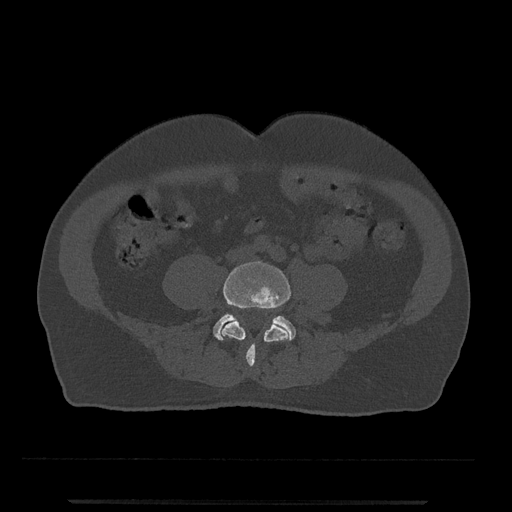
CT including the spine, one axial slice. Position 111 of 797 along the scan axis. 120 kVp. Bone window (W 1800 / L 400 HU). 0.5 mm slice thickness. 512 × 512 image matrix, field of view 419 × 419 mm. Male patient, age 63 years. From the clinical record (not read from this slice): primary cancer: prostate.
Outlined on this slice (semi-automatically segmented with operator editing):
- L4 vertebra: bounding box [x1, y1, x2, y2] px = [220, 261, 291, 368]
- L5 vertebra: [213, 314, 296, 340]